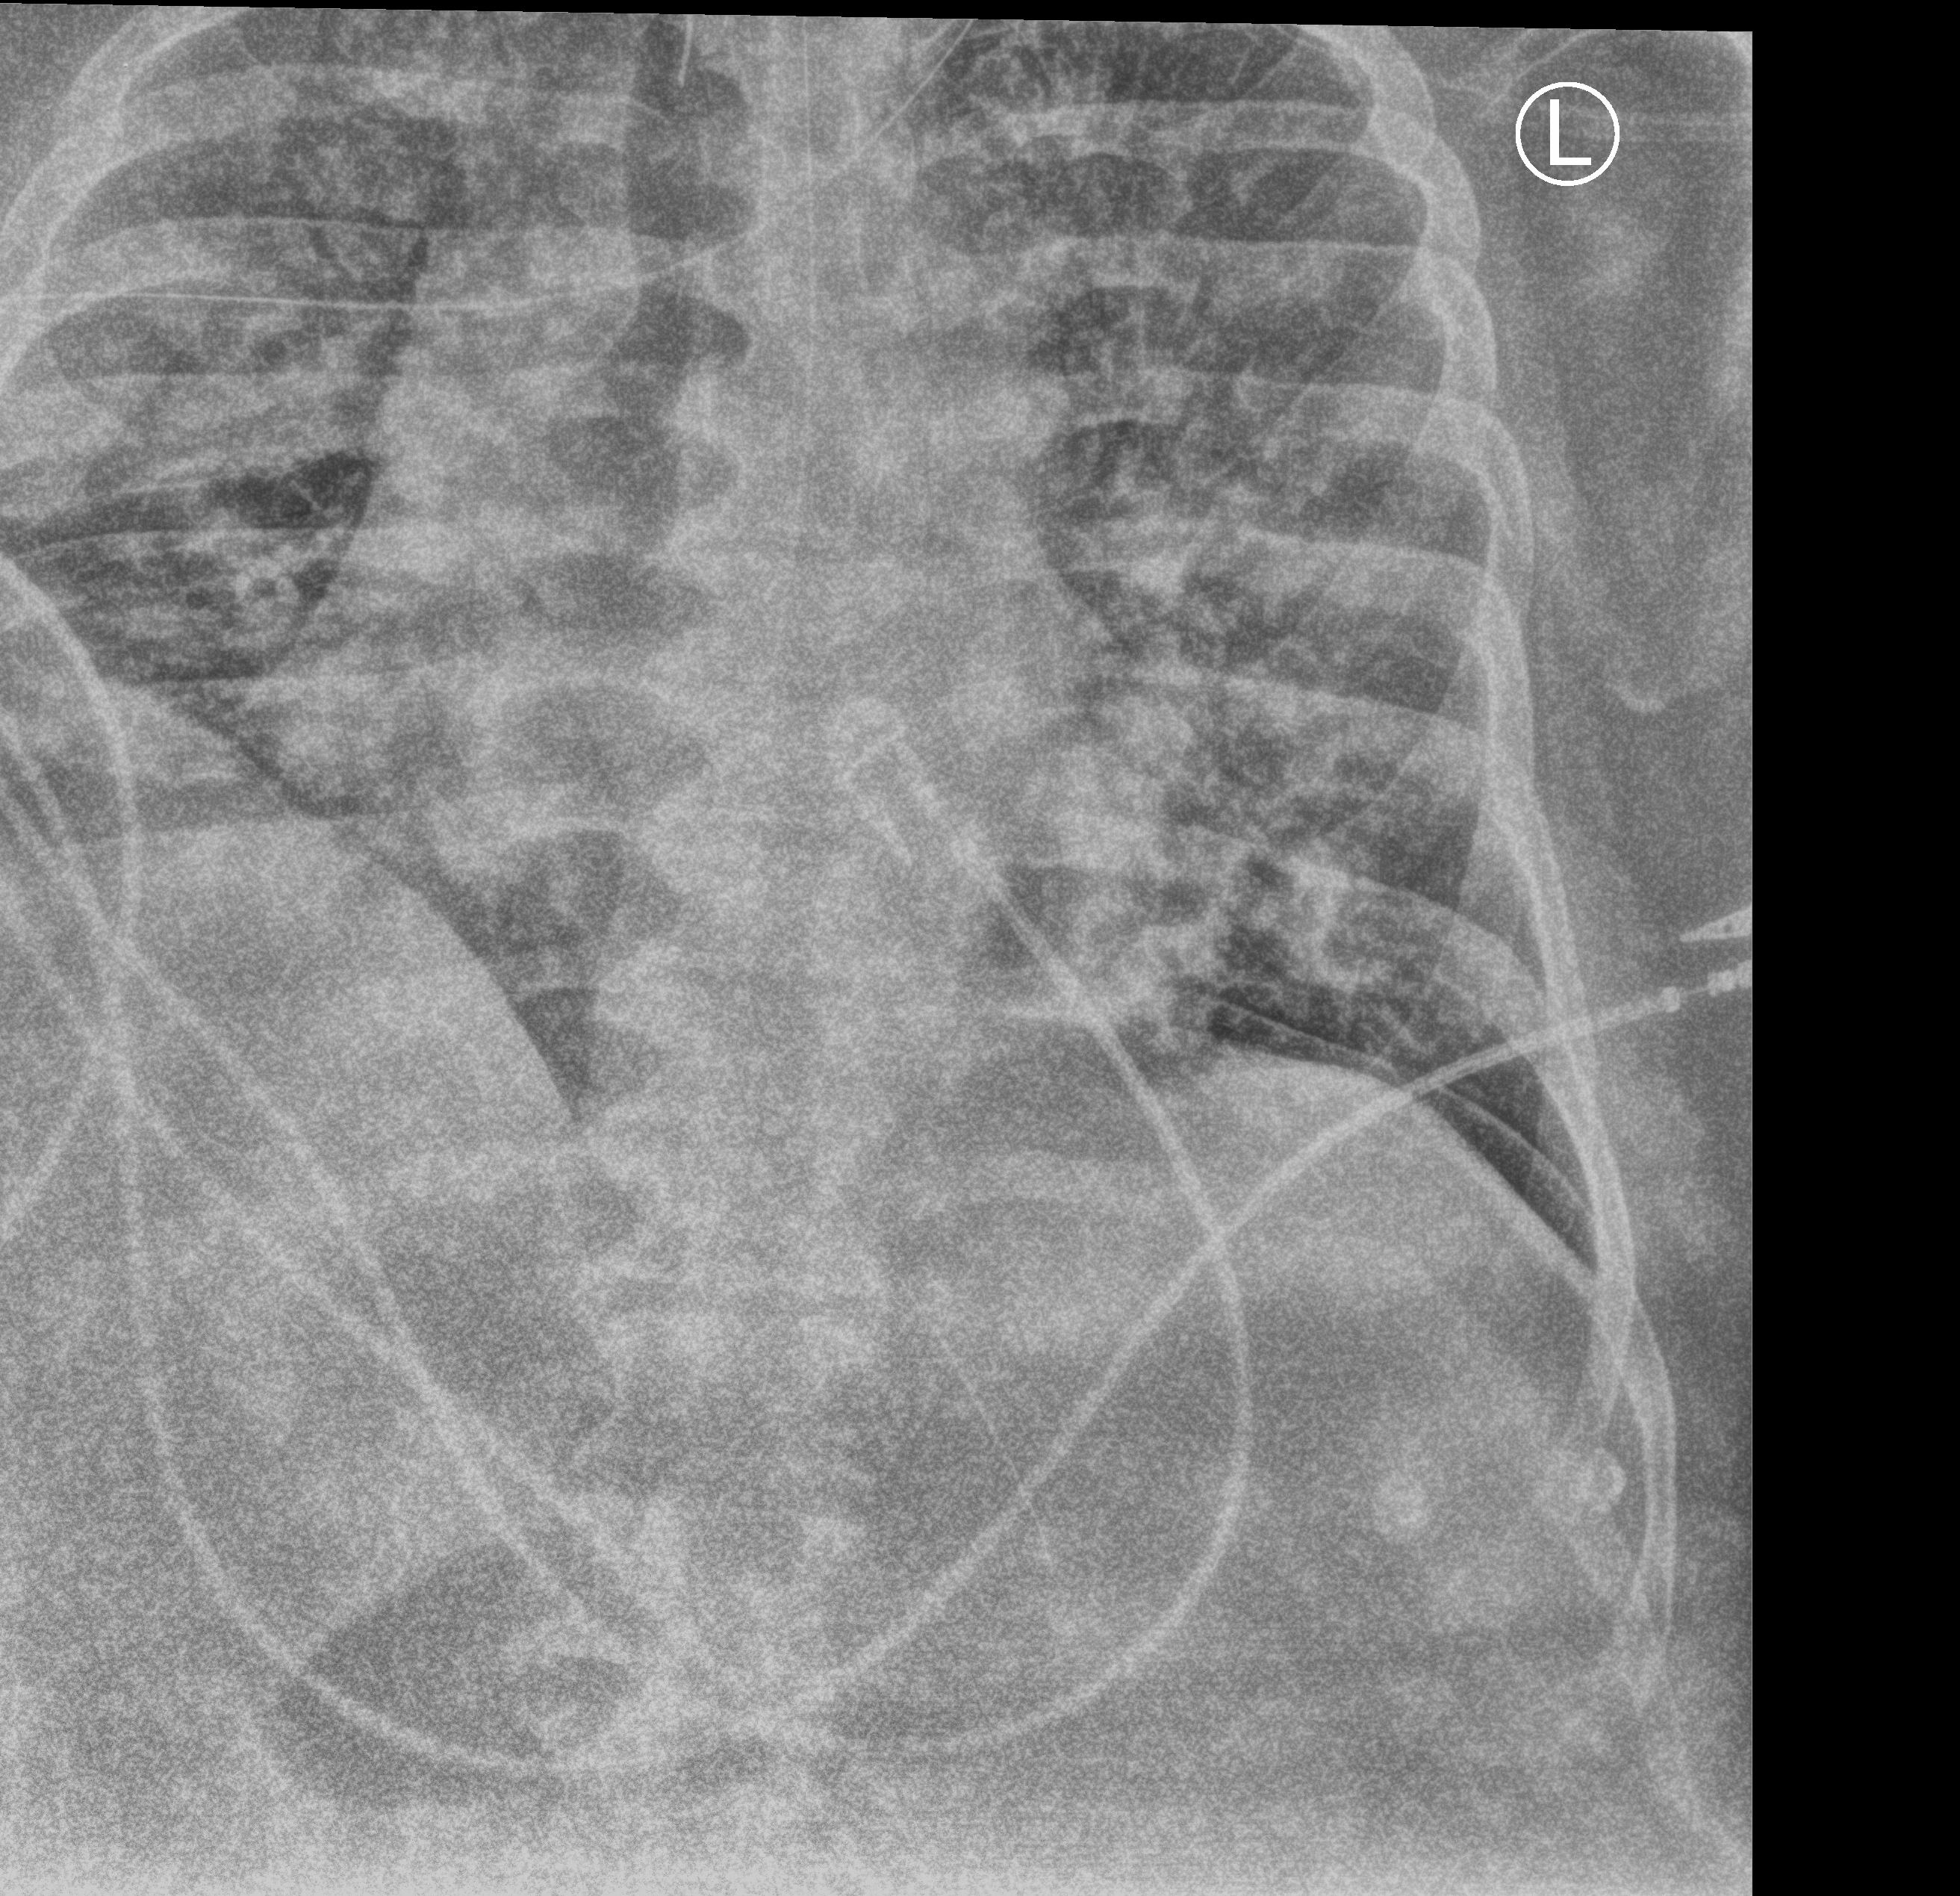
Bedside chest radiograph (computed radiography). Male patient hospitalised with COVID-19, age 18–59 years.
Admission-level facts for this patient (not findings on this image; timing relative to this image not recorded): admitted to intensive care during this hospital stay: yes; hypertension (admission record): yes.